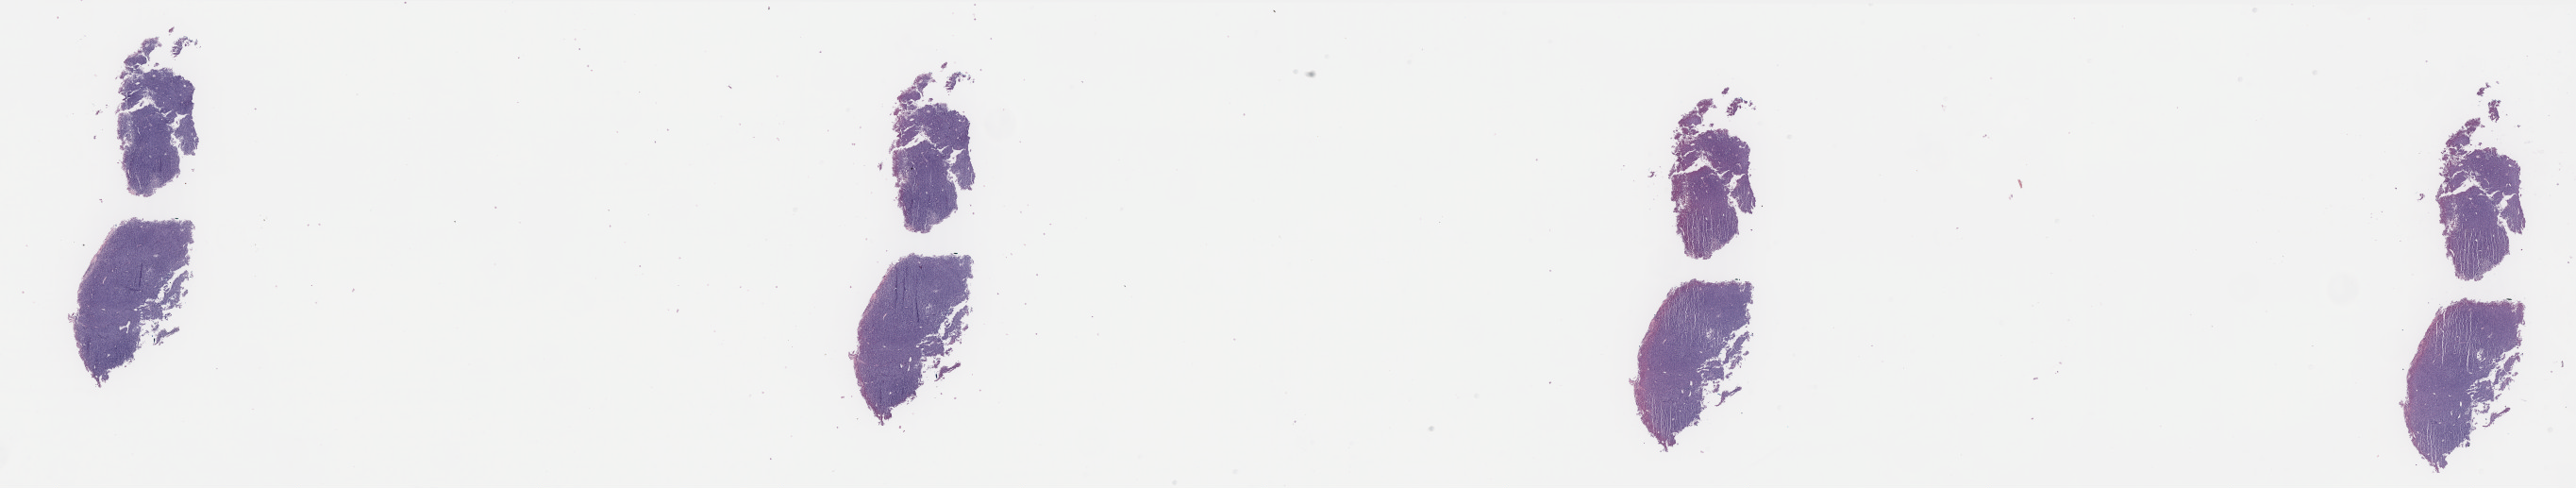
H&E whole-slide image — a low-resolution overview of the entire scanned area, about 43.8 x 8.3 mm. Formalin-fixed paraffin-embedded (FFPE) diagnostic section. Skin, primary tumour sample. Patient: male, age at initial diagnosis 42 years.
- histologic diagnosis: Malignant melanoma, NOS